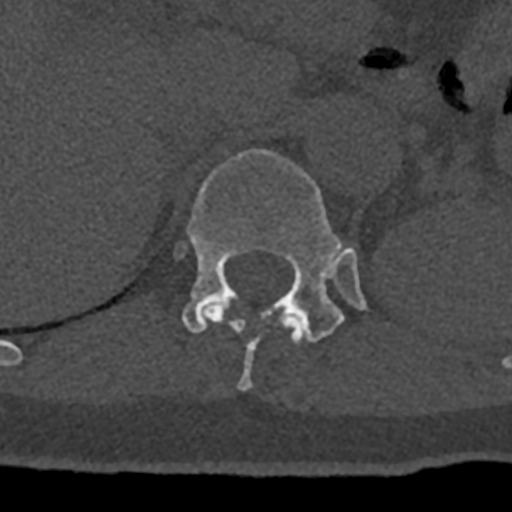
CT including the spine, one axial slice. Position 510 of 797 along the scan axis. Bone window (W 1800 / L 400 HU). 0.5 mm slice thickness. 512 × 512 image matrix, field of view 160 × 160 mm. Patient: male, 74 years. From the clinical record (not read from this slice): primary cancer: renal; vertebrae with lytic lesions (as recorded): T10, L1, L2, L3, L4, L5.
Structures marked on this image (semi-automatically segmented with operator editing):
- T11 vertebra: bounding box [x1, y1, x2, y2] px = [203, 301, 304, 391]
- T12 vertebra: [177, 149, 367, 343]